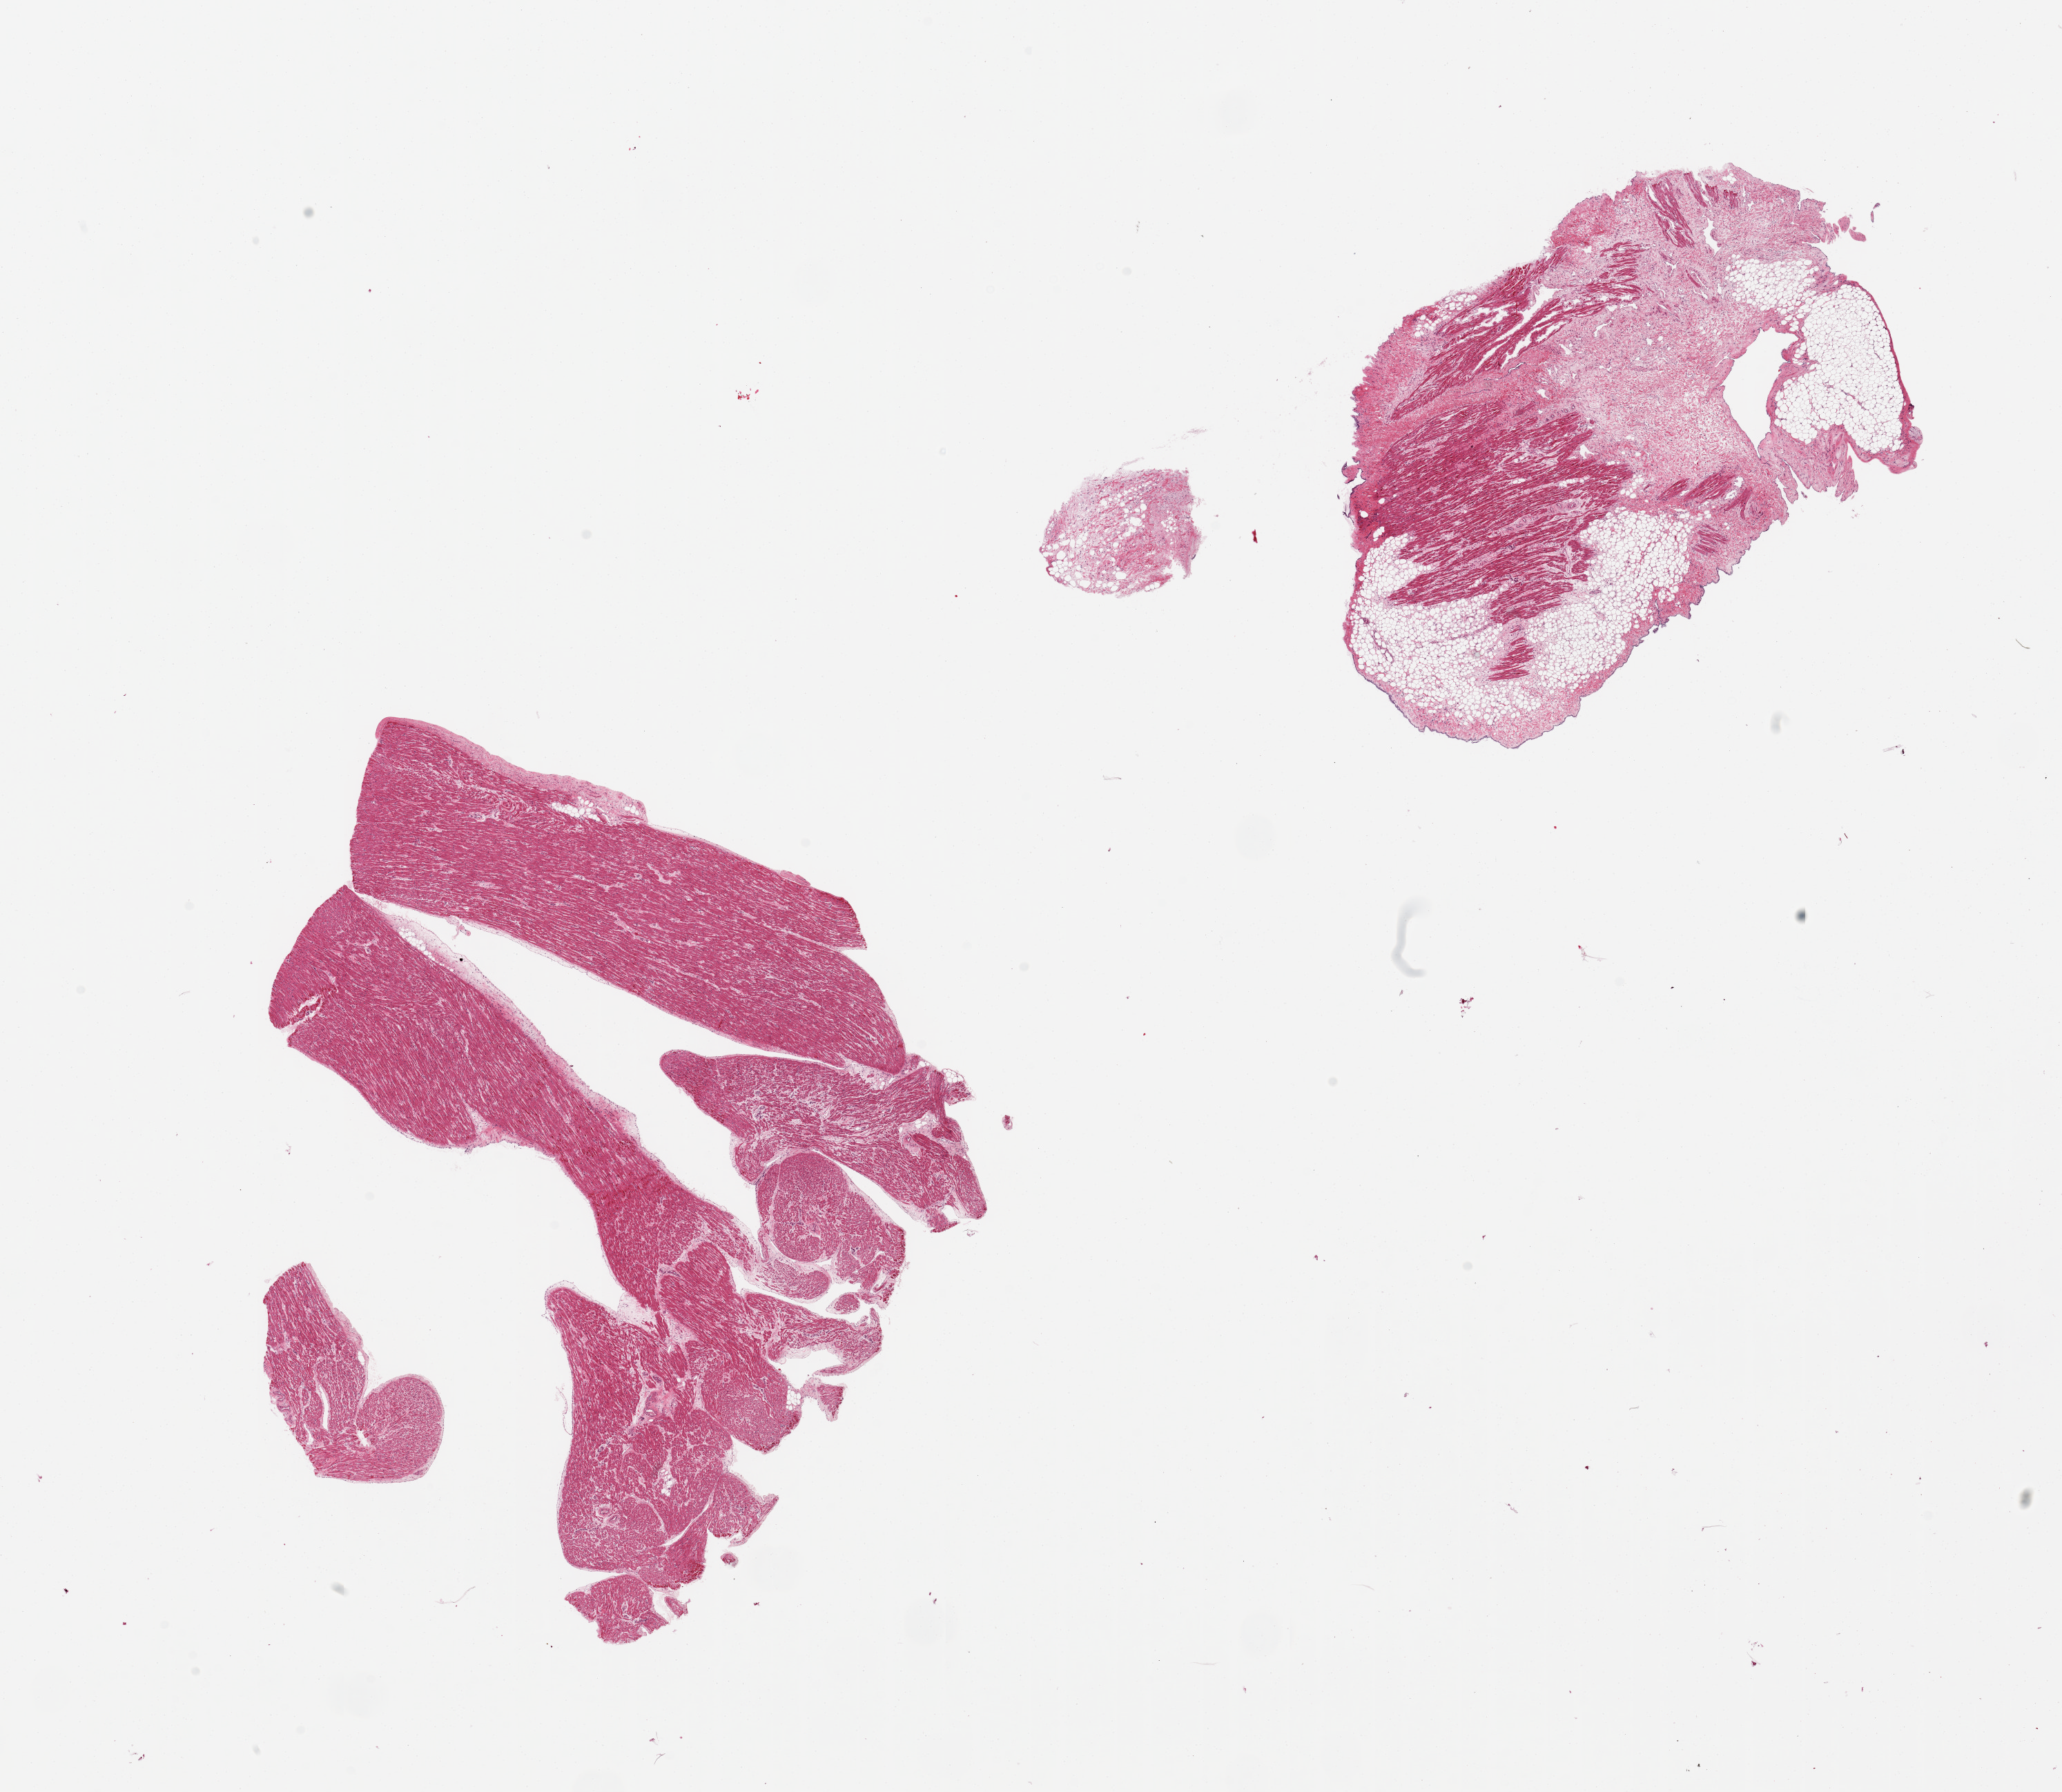
Whole-slide image, hematoxylin and eosin (H&E) stain, brightfield — whole scanned area (about 23.6 x 20.5 mm) shown as a low-resolution overview, PAXgene-fixed paraffin-embedded (PFPE) section, section of auricular appendage (target tissue), tissue donor sample. Donor: female.
• pathologist's review note for this sample: 2 pieces, one is ~50% fat/epicardium